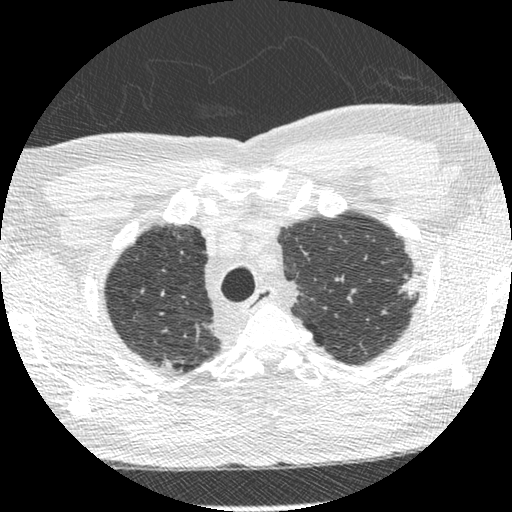
Low-dose screening chest CT, one axial slice. Slice 239 of 275 in the series (ordered by position). Reconstruction kernel STANDARD. 120 kVp. Lung window (W 1500 / L -600 HU). 1.25 mm slice thickness. 512 × 512 image matrix, field of view 330 × 330 mm.
Structures marked on this image (outlined manually by an expert reader):
- lesion 1 (tumor, upper lobe of left lung): box from (x=399, y=275) to (x=416, y=299) px